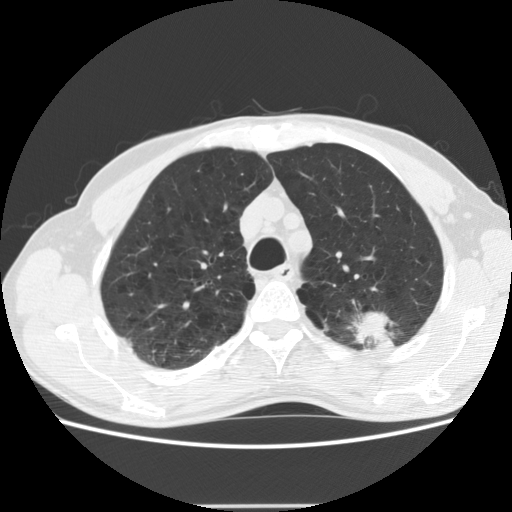
Low-dose screening chest CT, one axial slice; slice 150 of 191 in the series (ordered by position); reconstruction kernel STANDARD; 120 kVp; lung window (W 1500 / L -600 HU); 2.5 mm slice thickness; 512 × 512 image matrix, field of view 352 × 352 mm.
Structures marked on this image (manually delineated by an expert):
- lesion 1 (tumor, upper lobe of left lung): box from (x=353, y=312) to (x=392, y=344) px